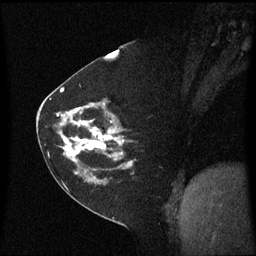
Breast MRI (dynamic contrast-enhanced), one sagittal slice. Position 34 of 60 along the scan axis. Dynamic contrast-enhanced series, image 2 of 3 at this slice position (ordered by acquisition). 1.5 T. TE 4.2 ms, TR 8.4 ms. 256 × 256 image matrix. Female patient, age 60 years. From the clinical record (not read from this slice): setting: breast cancer imaged before/during neoadjuvant chemotherapy; receptor status: triple-negative.
Outlined on this slice (semi-automatic segmentation, software-assisted and operator-edited):
- analysis volume of interest (the breast-tissue region the enhancement analysis was run in; not a lesion): box from (x=45, y=99) to (x=135, y=182) px
- tumour enhancement mask (voxels above the 70 % enhancement threshold inside the analysis volume of interest): (x=61, y=107)–(x=133, y=166)